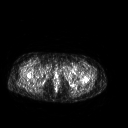
FDG PET of an extremity soft-tissue mass (from a PET/CT study), one axial slice. Position 256 of 267 along the scan axis. 128 × 128 image matrix, field of view 500 × 500 mm. Female patient, age 42 years. From the clinical record (not read from this slice): histological type: pleiomorphic leiomyosarcoma; grade: intermediate; site of the primary tumour: left thigh.
Annotated regions visible in this slice (expert contour drawn on MRI and transferred to this co-registered scan by the dataset authors):
- gross tumour volume including surrounding oedema: bounding box <61,64,78,77> (left, top, right, bottom; pixels)
- gross tumour volume (mass): <67,66,77,76>